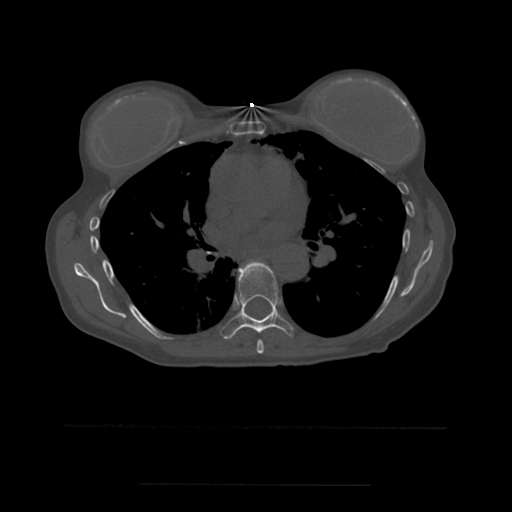
CT including the spine, one axial slice. Slice 361 of 544 in the series (ordered by position). Bone window (W 1800 / L 400 HU). 512 × 512 image matrix, field of view 350 × 350 mm. Patient age 58 years. Case-level facts recorded for this patient, not image findings: primary cancer: lung.
Annotated regions visible in this slice (semi-automatic segmentation, software-assisted and operator-edited):
- T6 vertebra: bounding box (x1, y1, x2, y2) in pixels: (257, 340, 264, 354)
- T7 vertebra: (221, 260, 294, 340)